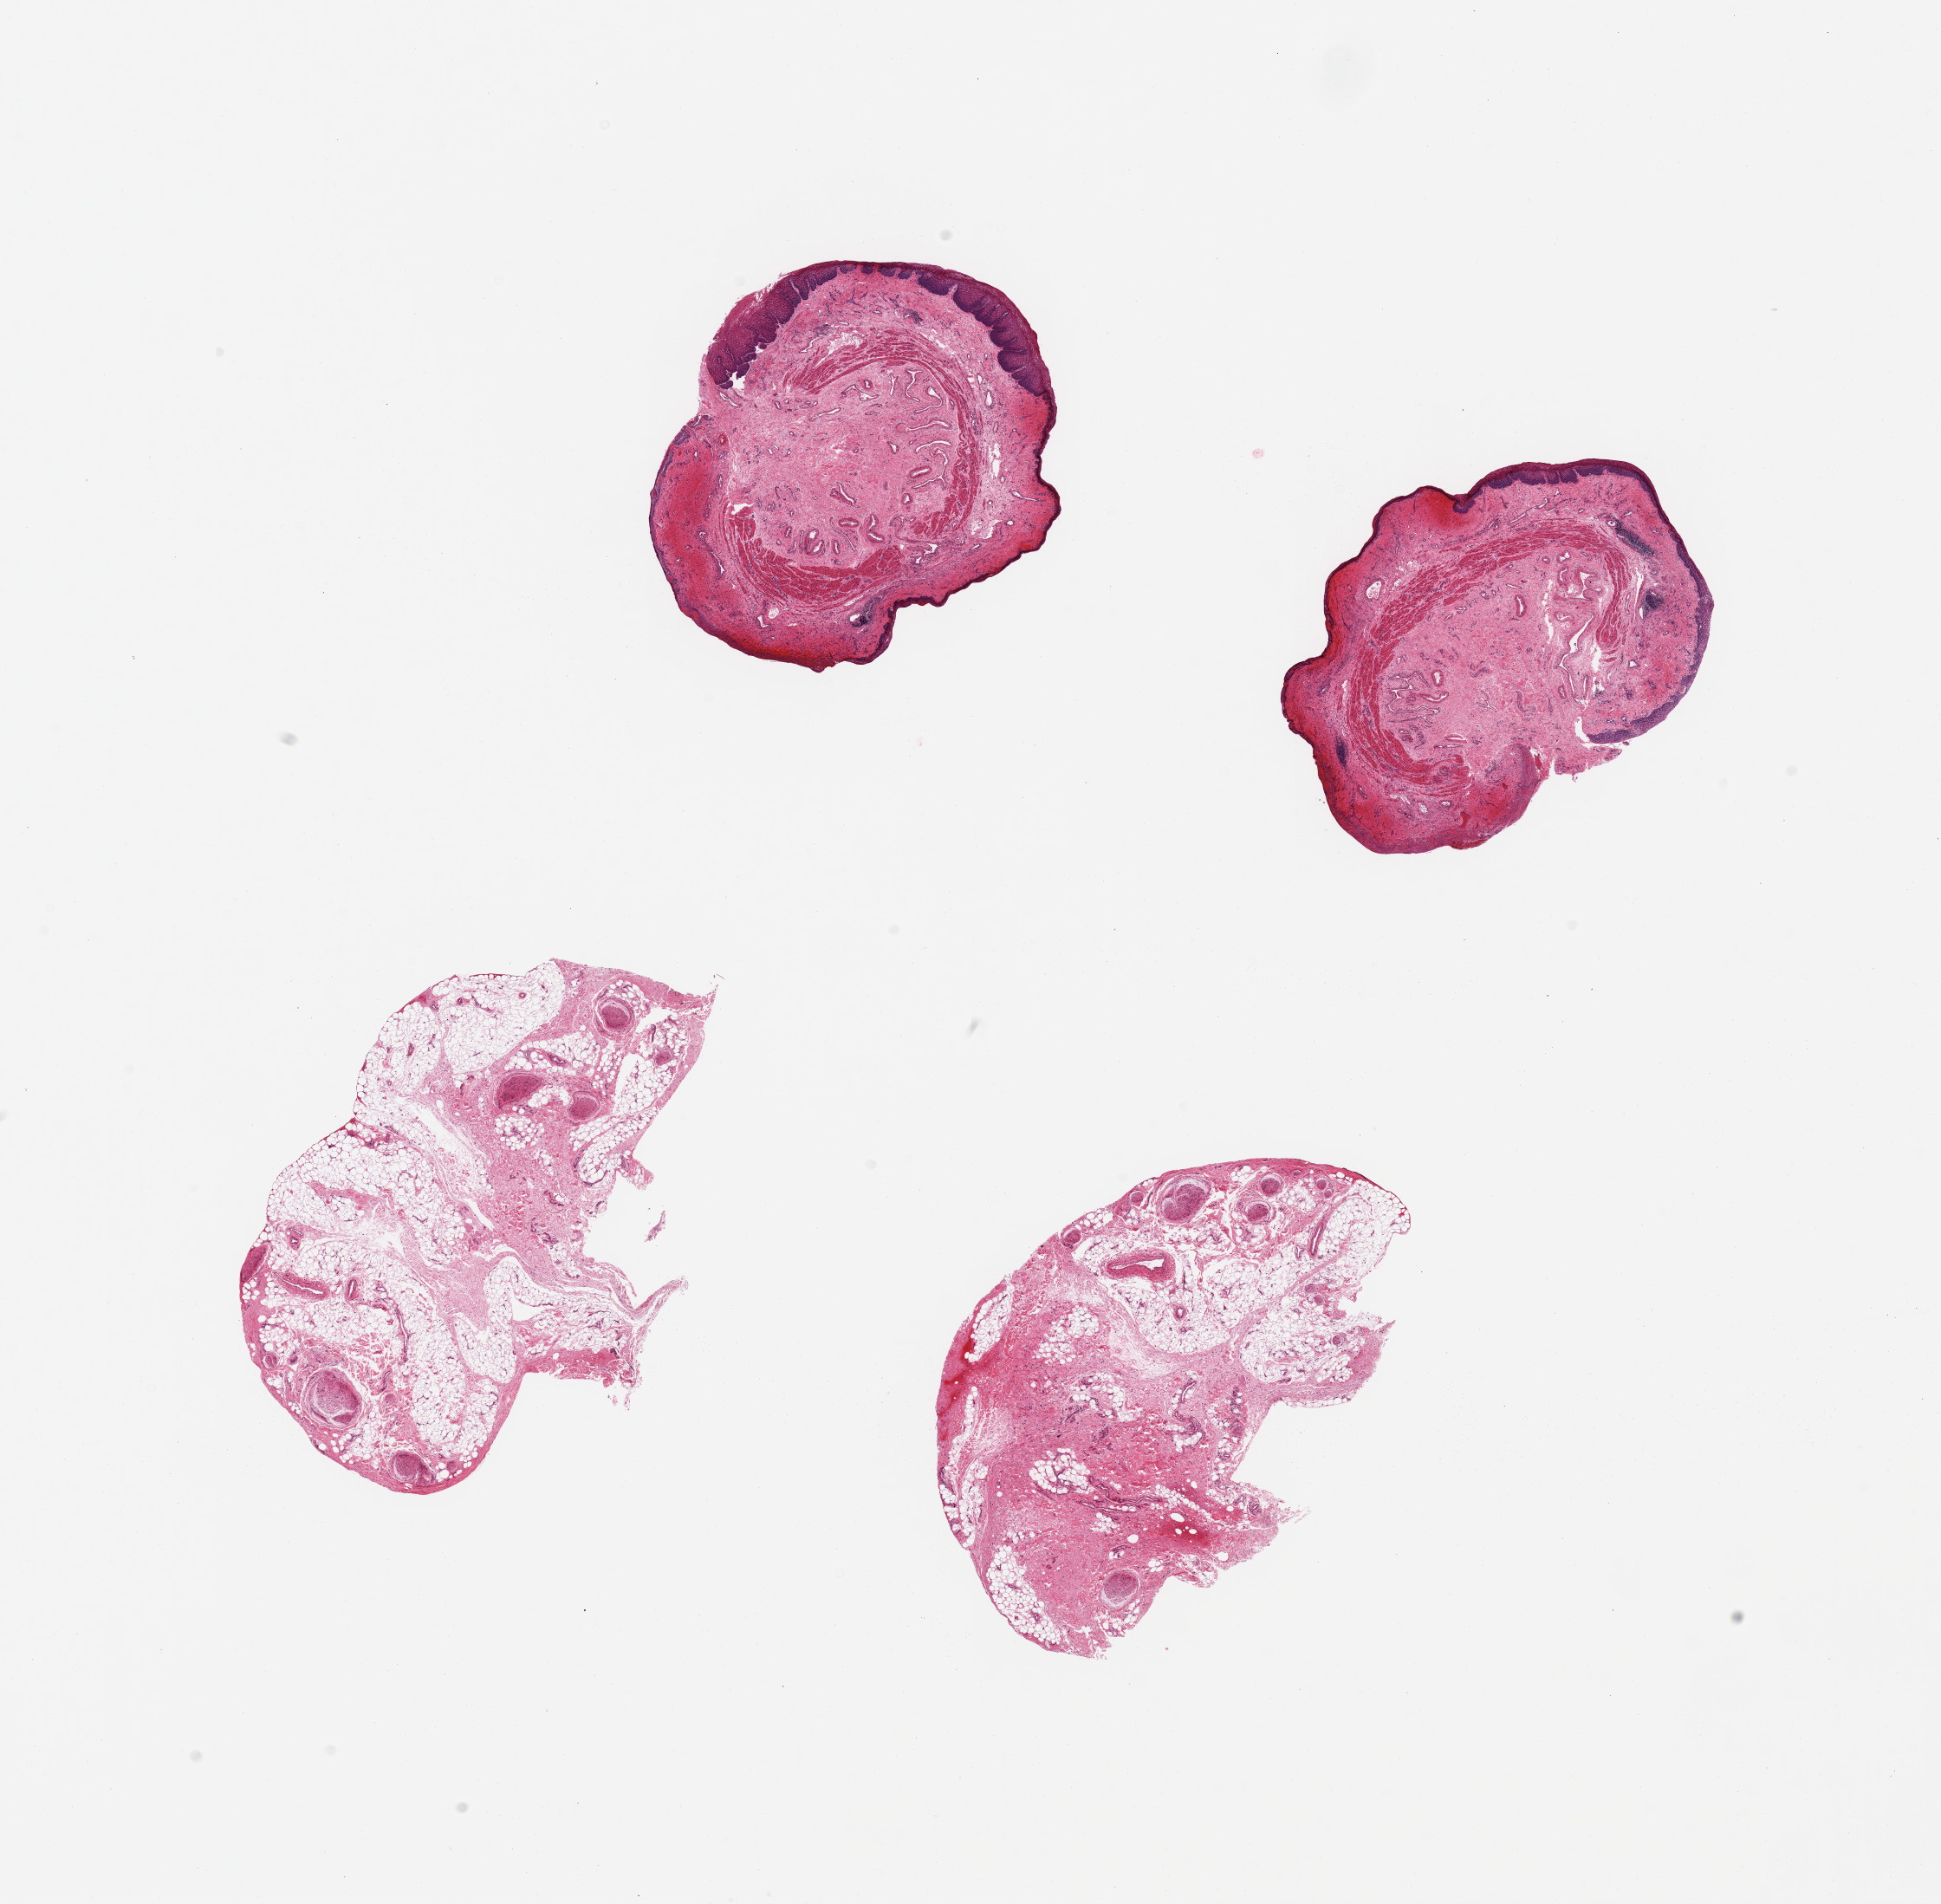
H&E whole-slide image, low-resolution overview of the scanned area, about 17.7 x 17.4 mm, PAXgene-fixed, paraffin-embedded tissue, section of esophageal mucous membrane (target tissue), donor tissue sample. Male donor.
Reviewer comment on this tissue sample: 4 pieces, 2 with squamous mucosa, rest is fat/unknown provenance.